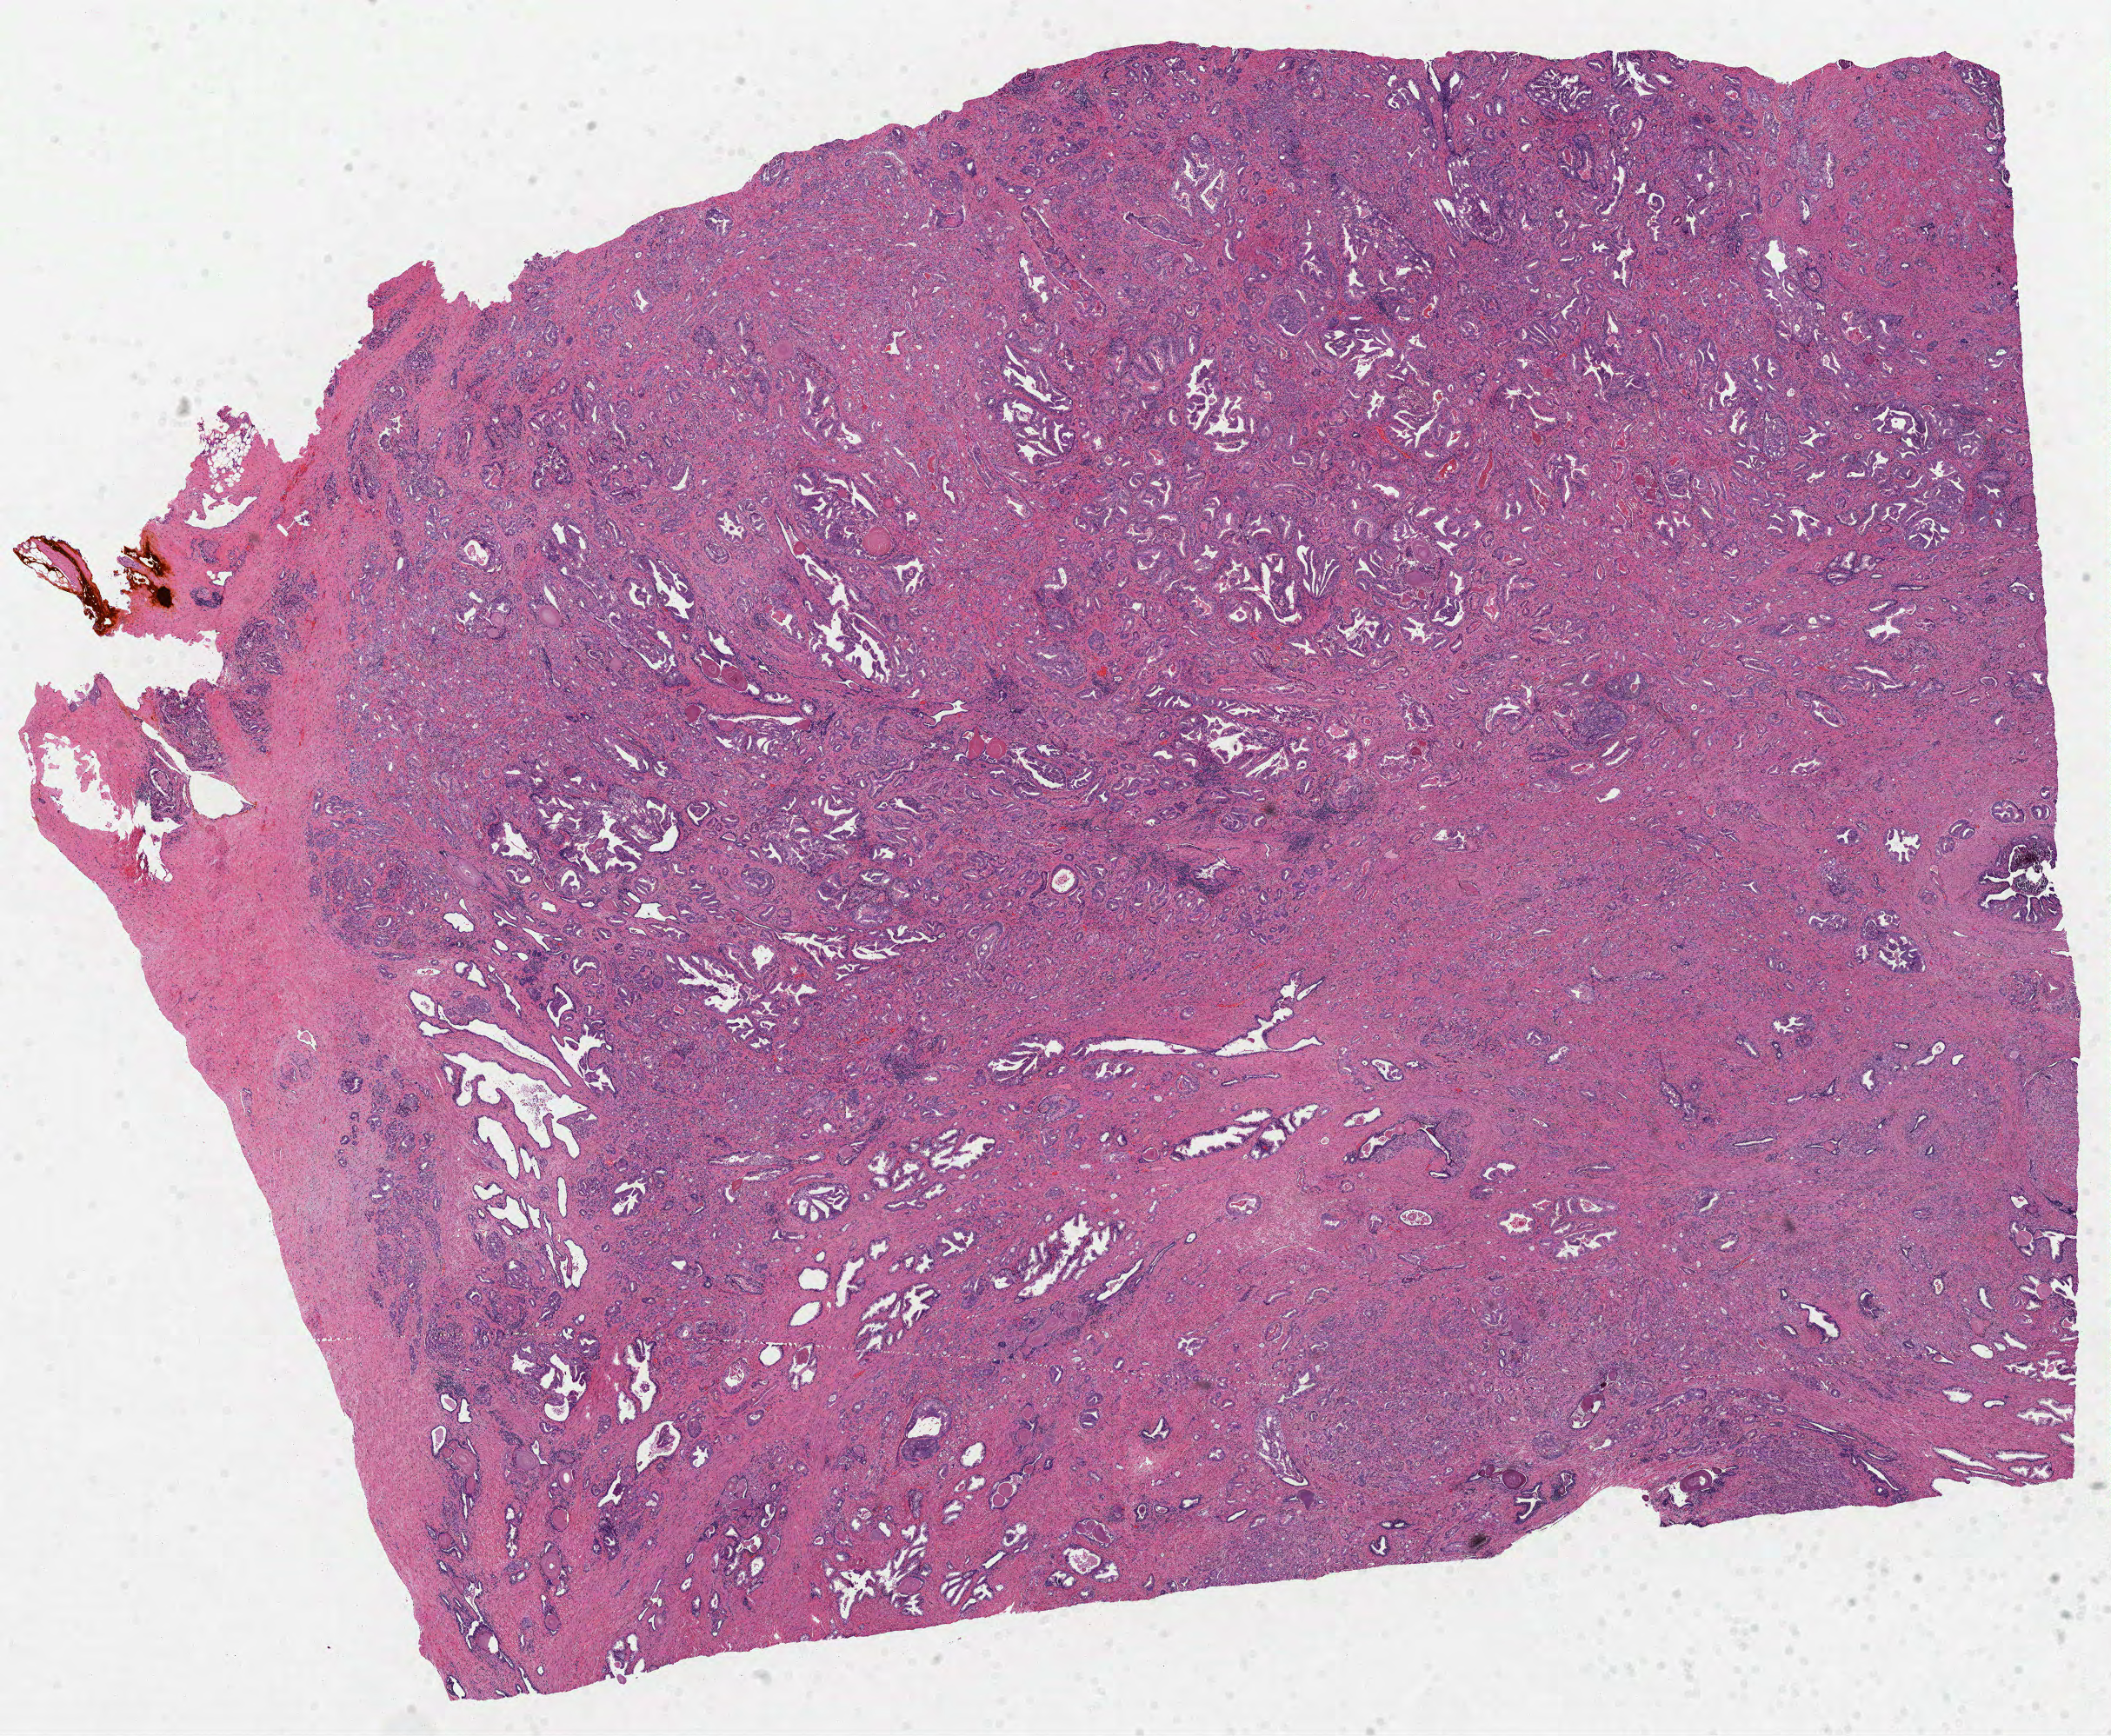
Digitized Hematoxylin and eosin (H&E) stained tissue section (whole slide), low-resolution overview of the scanned area, about 19.6 x 16.1 mm (slide scanned at 40x), FFPE section, prostate, primary tumour sample. Male, age 54 years at initial diagnosis. Gleason score: 9 (4+5).
Lymph nodes positive (case pathology): 2 of 21 examined. Histologic diagnosis: Acinar cell carcinoma.